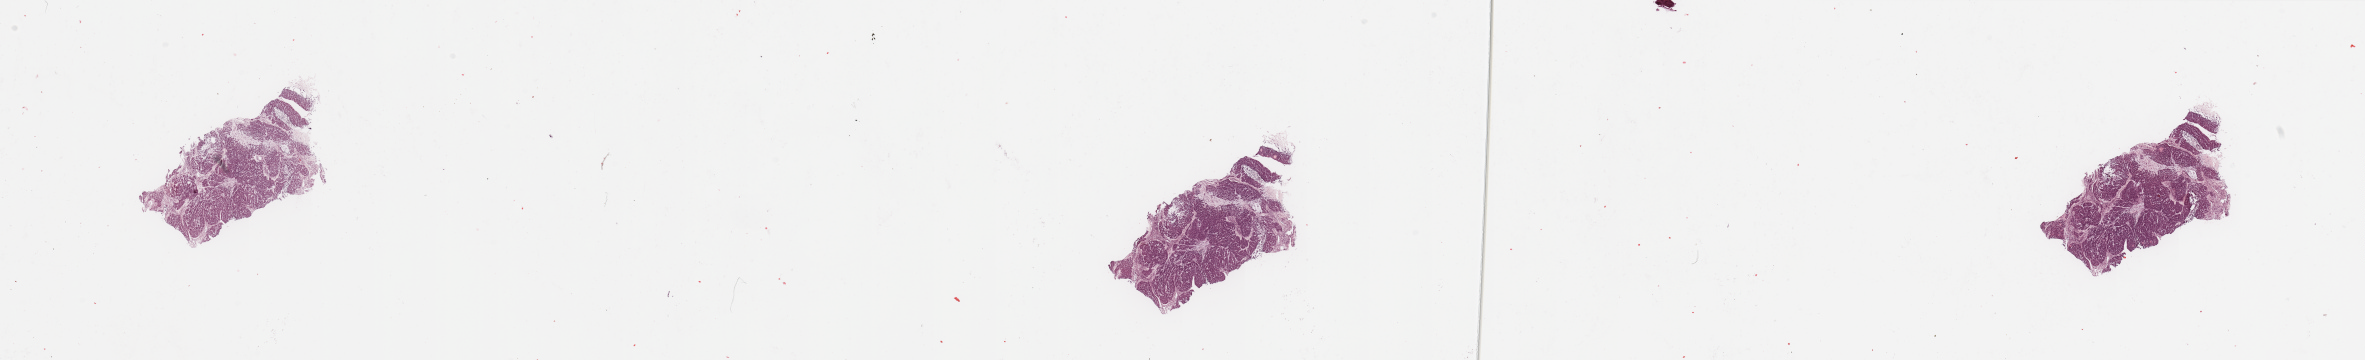
H&E whole-slide image — low-resolution overview of the scanned area, about 37.4 x 5.7 mm (slide scanned at 20x), tumour tissue sample, sampled site: larynx. Male, 68 y/o. Pathologist review of this section (percent, as recorded): tumour nuclei 90%, necrosis 5%.
Histologic diagnosis: Squamous cell carcinoma, NOS (larynx, NOS).